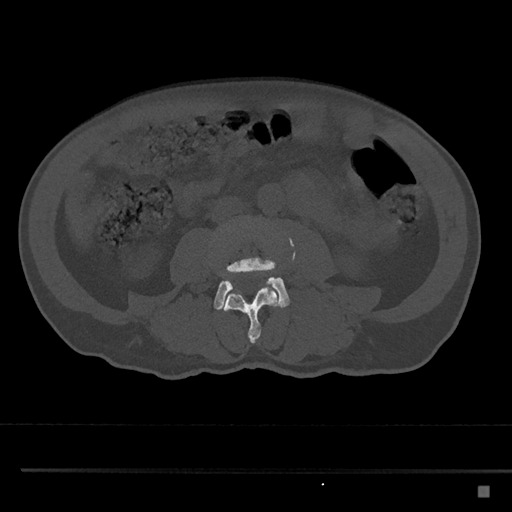
CT including the spine, one axial slice. Bone window (W 1800 / L 400 HU). 512 × 512 image matrix, field of view 391 × 391 mm. Patient: male, 59 years. Case-level facts recorded for this patient, not image findings: primary cancer: prostate.
Structures marked on this image (semi-automatic segmentation, software-assisted and operator-edited):
- L3 vertebra: bounding box (x1, y1, x2, y2) in pixels: (222, 280, 281, 343)
- L4 vertebra: (213, 235, 290, 310)